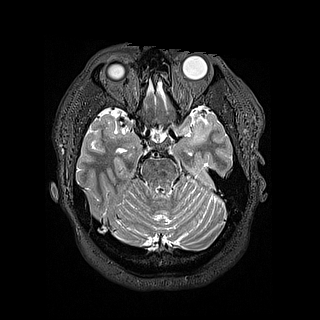
Brain MRI from a brain-tumour surgery series, one axial slice; slice 104 of 144 in the series (ordered by position); 1.2 mm slice thickness; 320 × 320 image matrix, field of view 254 × 254 mm. From the clinical record (not read from this slice): histopathology: Astrocytoma; WHO grade: 2; IDH mutation: yes.
Annotated regions visible in this slice (outlined manually by an expert reader):
- tumour: bounding box (x1, y1, x2, y2) in pixels: (188, 121, 203, 146)